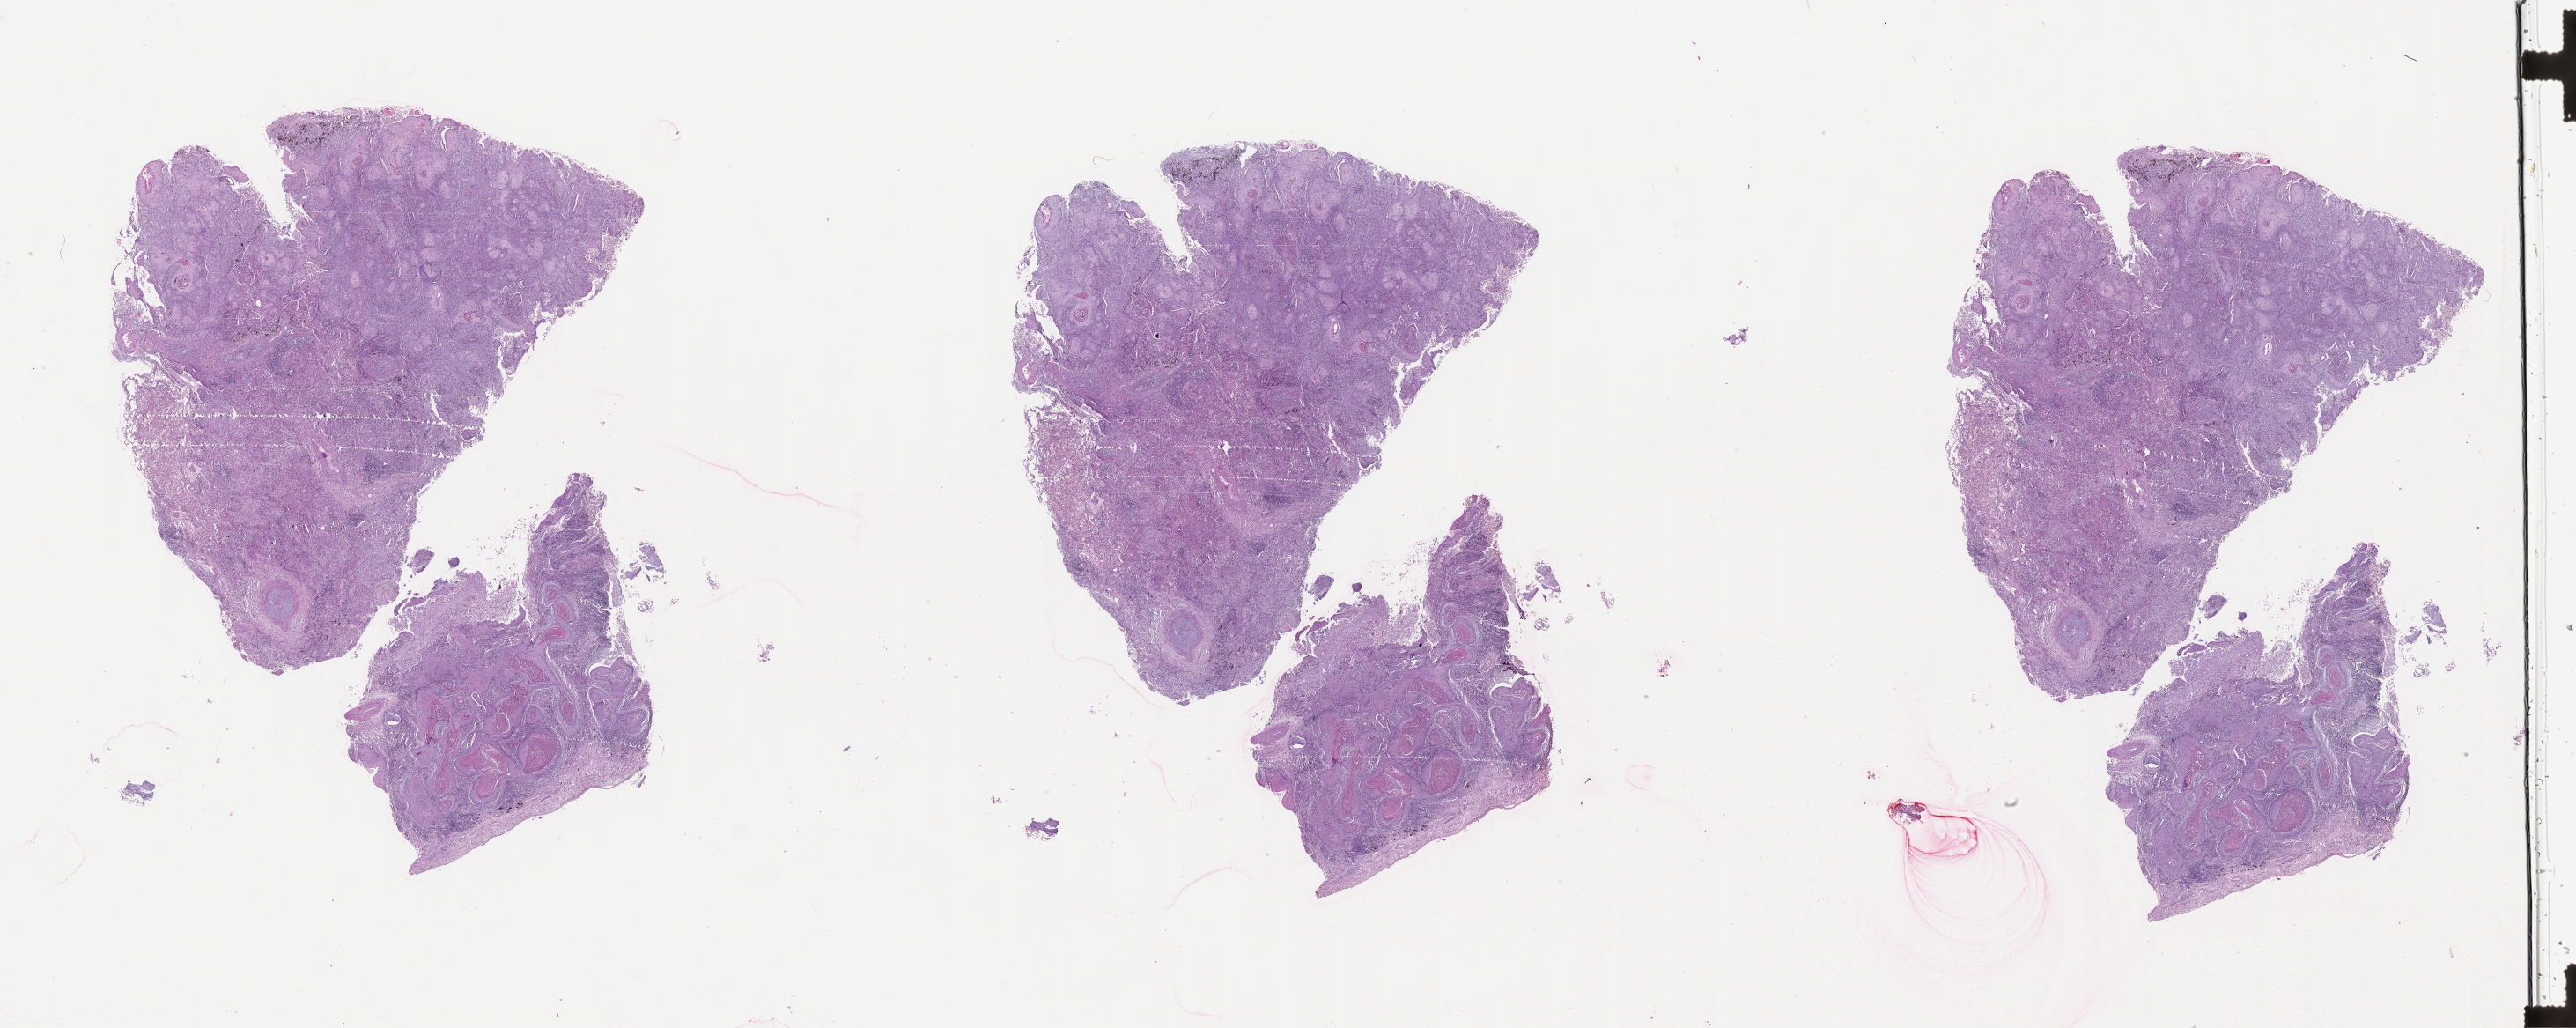
Whole-slide histology image, H&E — a low-resolution overview of the entire scanned area, about 47.1 x 18.8 mm (from a 20x scan), lung, tumour tissue. Male, 72 y/o.
Patient diagnosis (cohort enrolment): squamous cell carcinoma (lung).